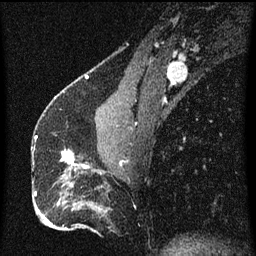
Breast MRI (dynamic contrast-enhanced), one sagittal slice; position 27 of 60 along the scan axis; dynamic contrast-enhanced series, image 2 of 3 at this slice position (ordered by acquisition); 1.5 T; TE 4.2 ms, TR 8 ms; 2 mm slice thickness; 256 × 256 image matrix, field of view 180 × 180 mm. Female patient, age 51 years.
Outlined on this slice (semi-automatic segmentation, software-assisted and operator-edited):
- analysis volume of interest (the breast-tissue region the enhancement analysis was run in; not a lesion): bounding box [x1, y1, x2, y2] px = [62, 150, 93, 175]
- tumour enhancement mask (voxels above the 70 % enhancement threshold inside the analysis volume of interest): [62, 150, 89, 169]